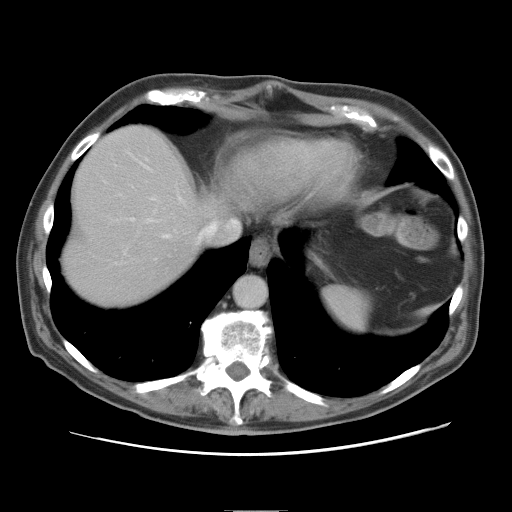
Contrast-enhanced abdominal CT, one axial slice; position 69 of 89 along the scan axis; 120 kVp; soft-tissue window (W 400 / L 40 HU); 5 mm slice thickness; 512 × 512 image matrix. Male patient, age 69 years. Case-level facts recorded for this patient, not image findings: diagnosis: colorectal cancer liver metastases, imaged before liver resection; multiple liver metastases: no; largest metastasis: 8.5 cm; chemotherapy before resection: no.
Structures marked on this image (expert manual segmentation):
- hepatic veins: bounding box [x1, y1, x2, y2] px = [146, 169, 239, 244]
- liver: [61, 126, 211, 310]
- planned liver remnant (the part of the liver to remain after resection): [61, 126, 214, 311]
- portal vein (with intrahepatic branches): [129, 218, 156, 223]